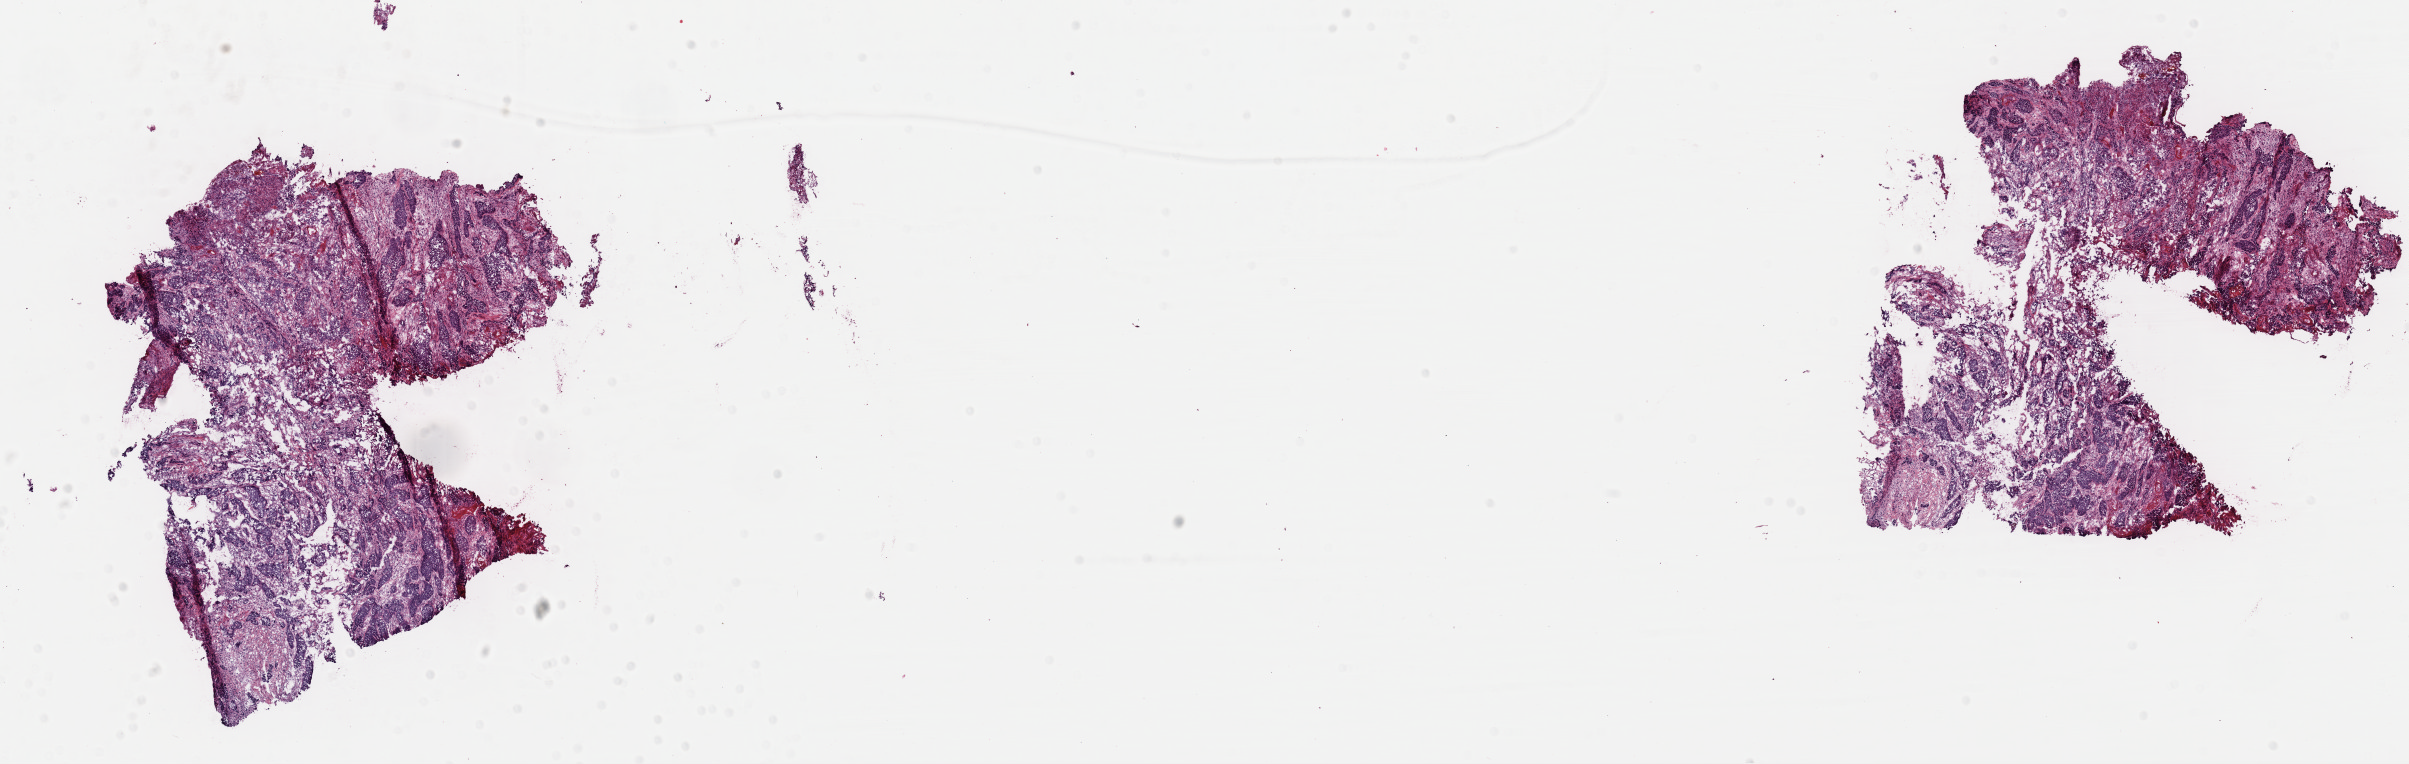
H&E whole-slide image — a low-resolution overview of the entire scanned area, about 19.0 x 6.0 mm, frozen section, cervix, primary tumour sample. Female patient; age at initial diagnosis 47 years. Histologic grade: G3 (poorly differentiated). Pathologist review of this section (percent, as recorded): tumour cells 40%, tumour nuclei 60%, normal cells 30%, stromal cells 25%, necrosis 5%. Infiltration values recorded for this section: lymphocyte infiltration 10%, monocyte infiltration 1%, neutrophil infiltration 0%.
FIGO stage: IIIB. Pathologic diagnosis: Squamous cell carcinoma, NOS (cervix uteri).